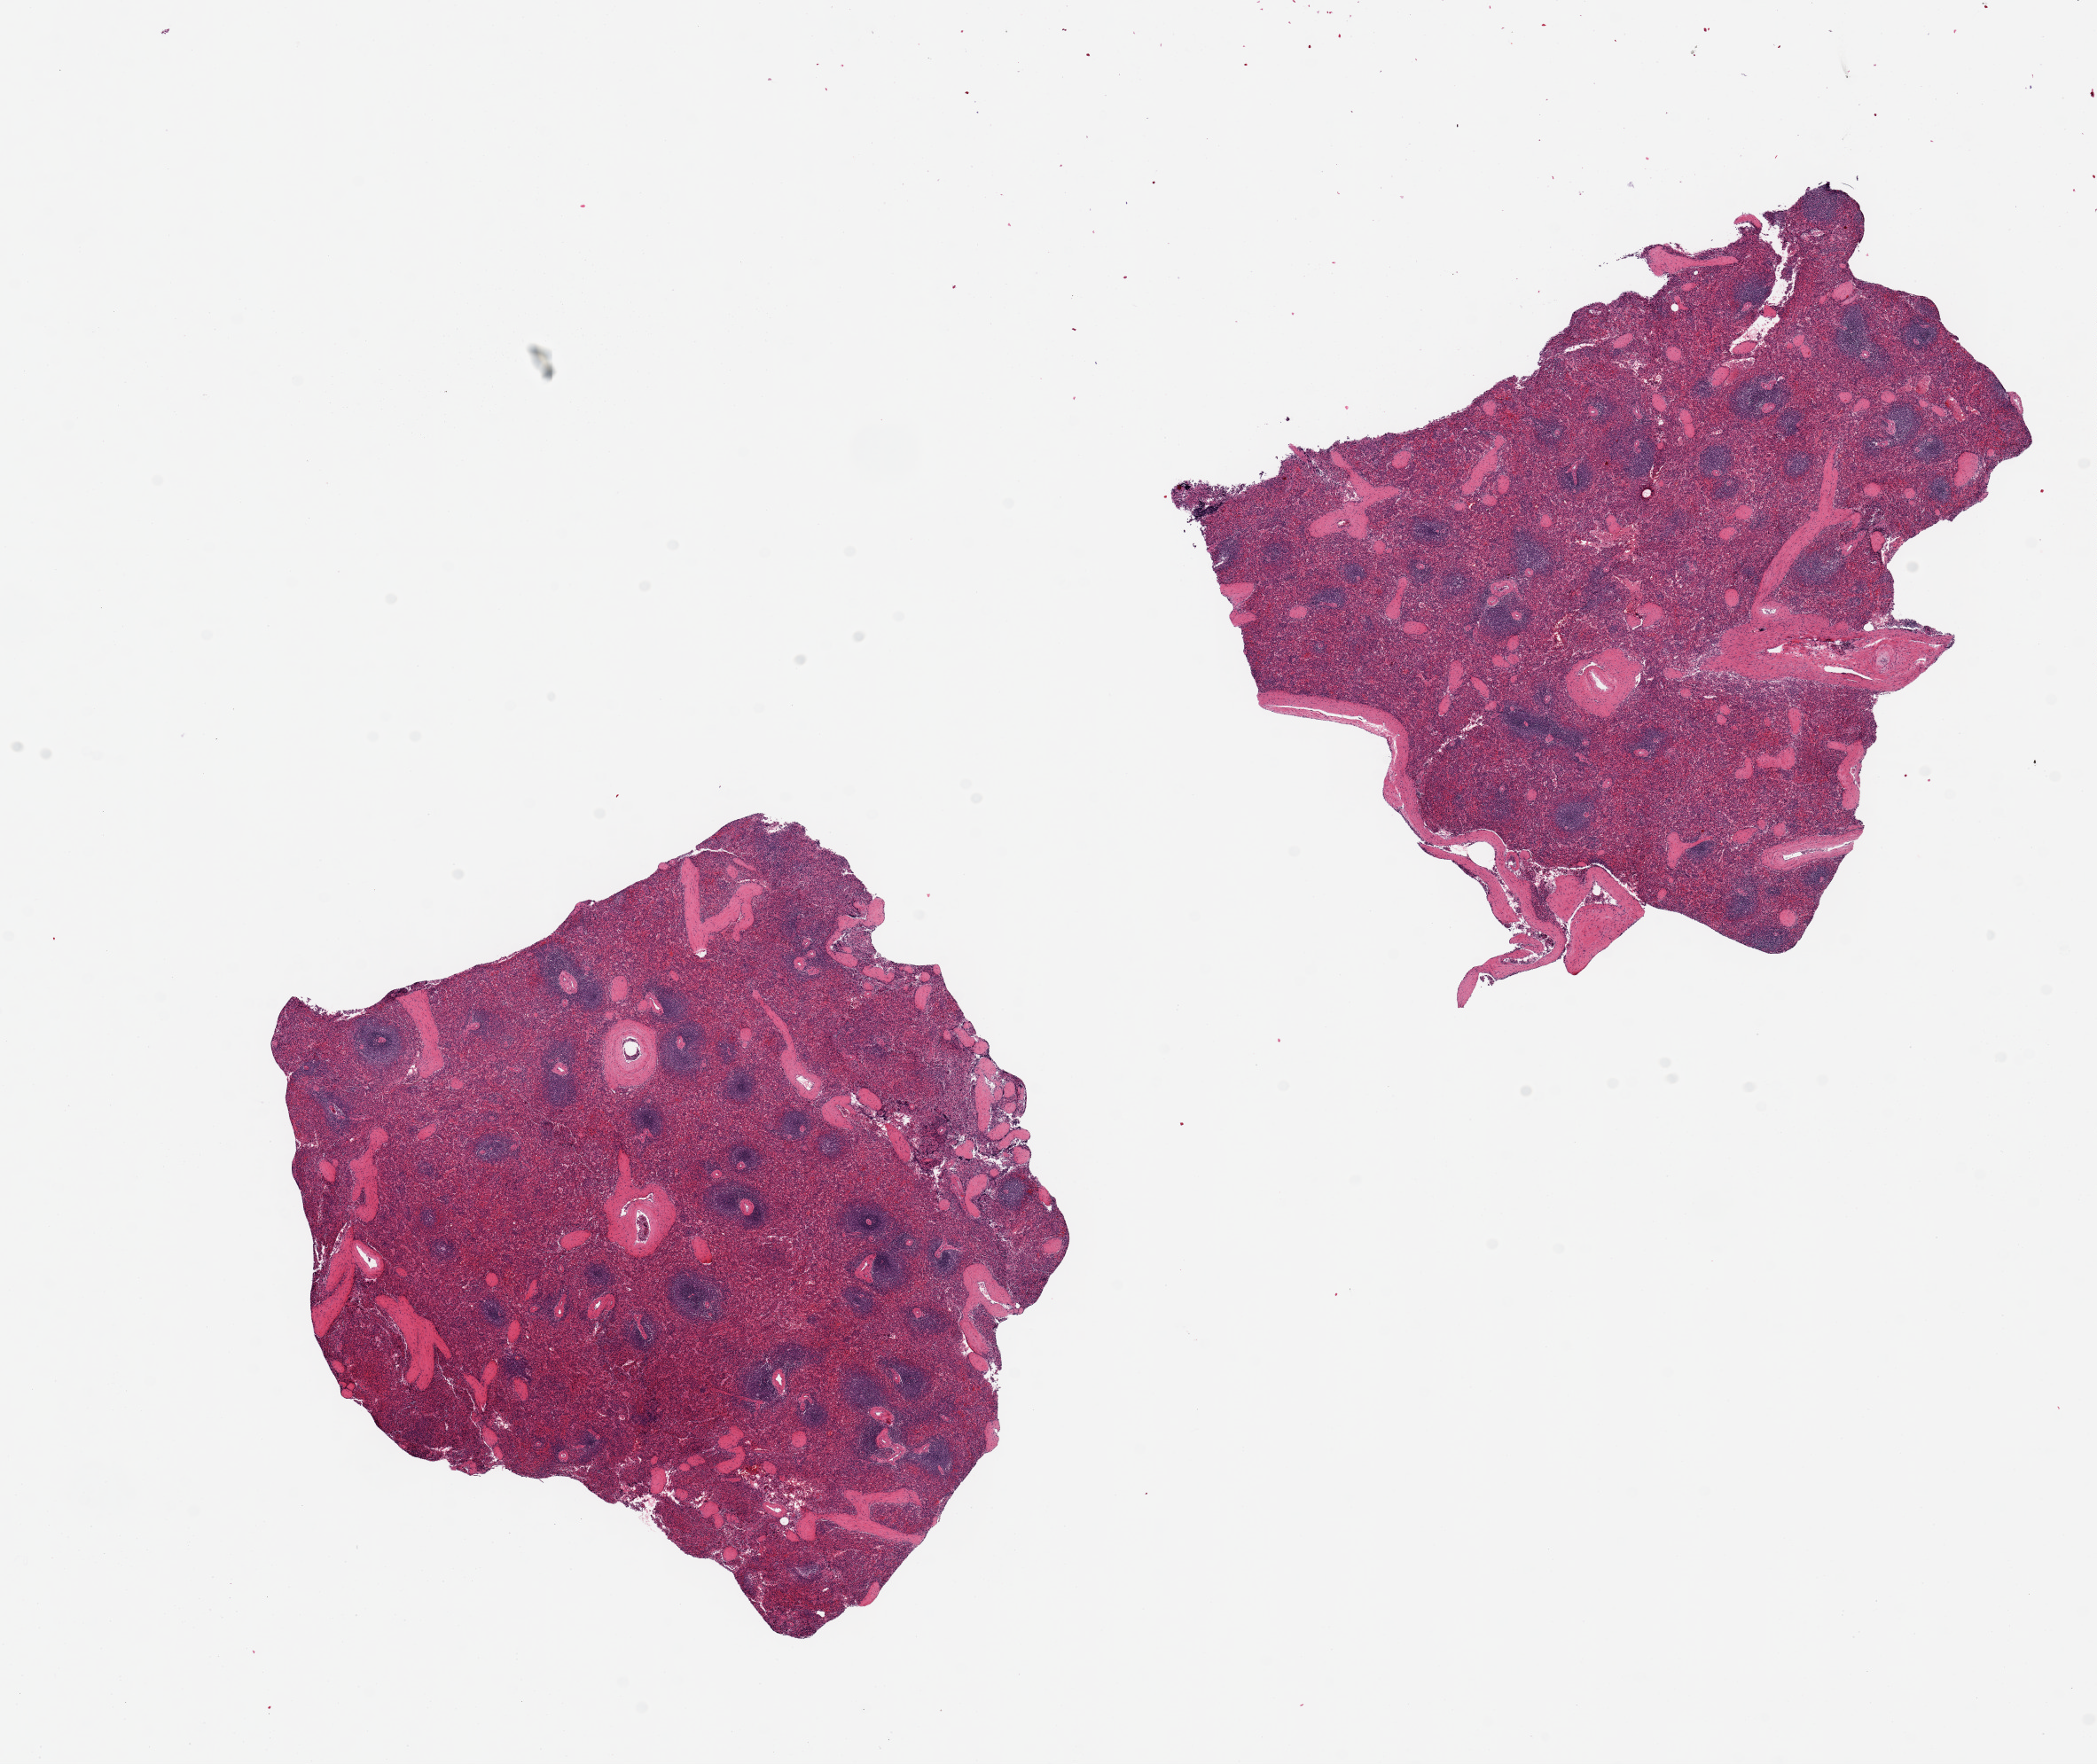
Digitized hematoxylin and eosin (H&E)-stained section, brightfield — a low-resolution overview of the entire scanned area, about 18.7 x 15.7 mm (slide scanned at 20x); PAXgene-fixed paraffin-embedded (PFPE) section; target tissue: spleen; donor tissue sample. Donor: male.
- pathologist's review note for this sample: 2 pieces, 7x6.5 & 8x7mm; balanced red and white pulp